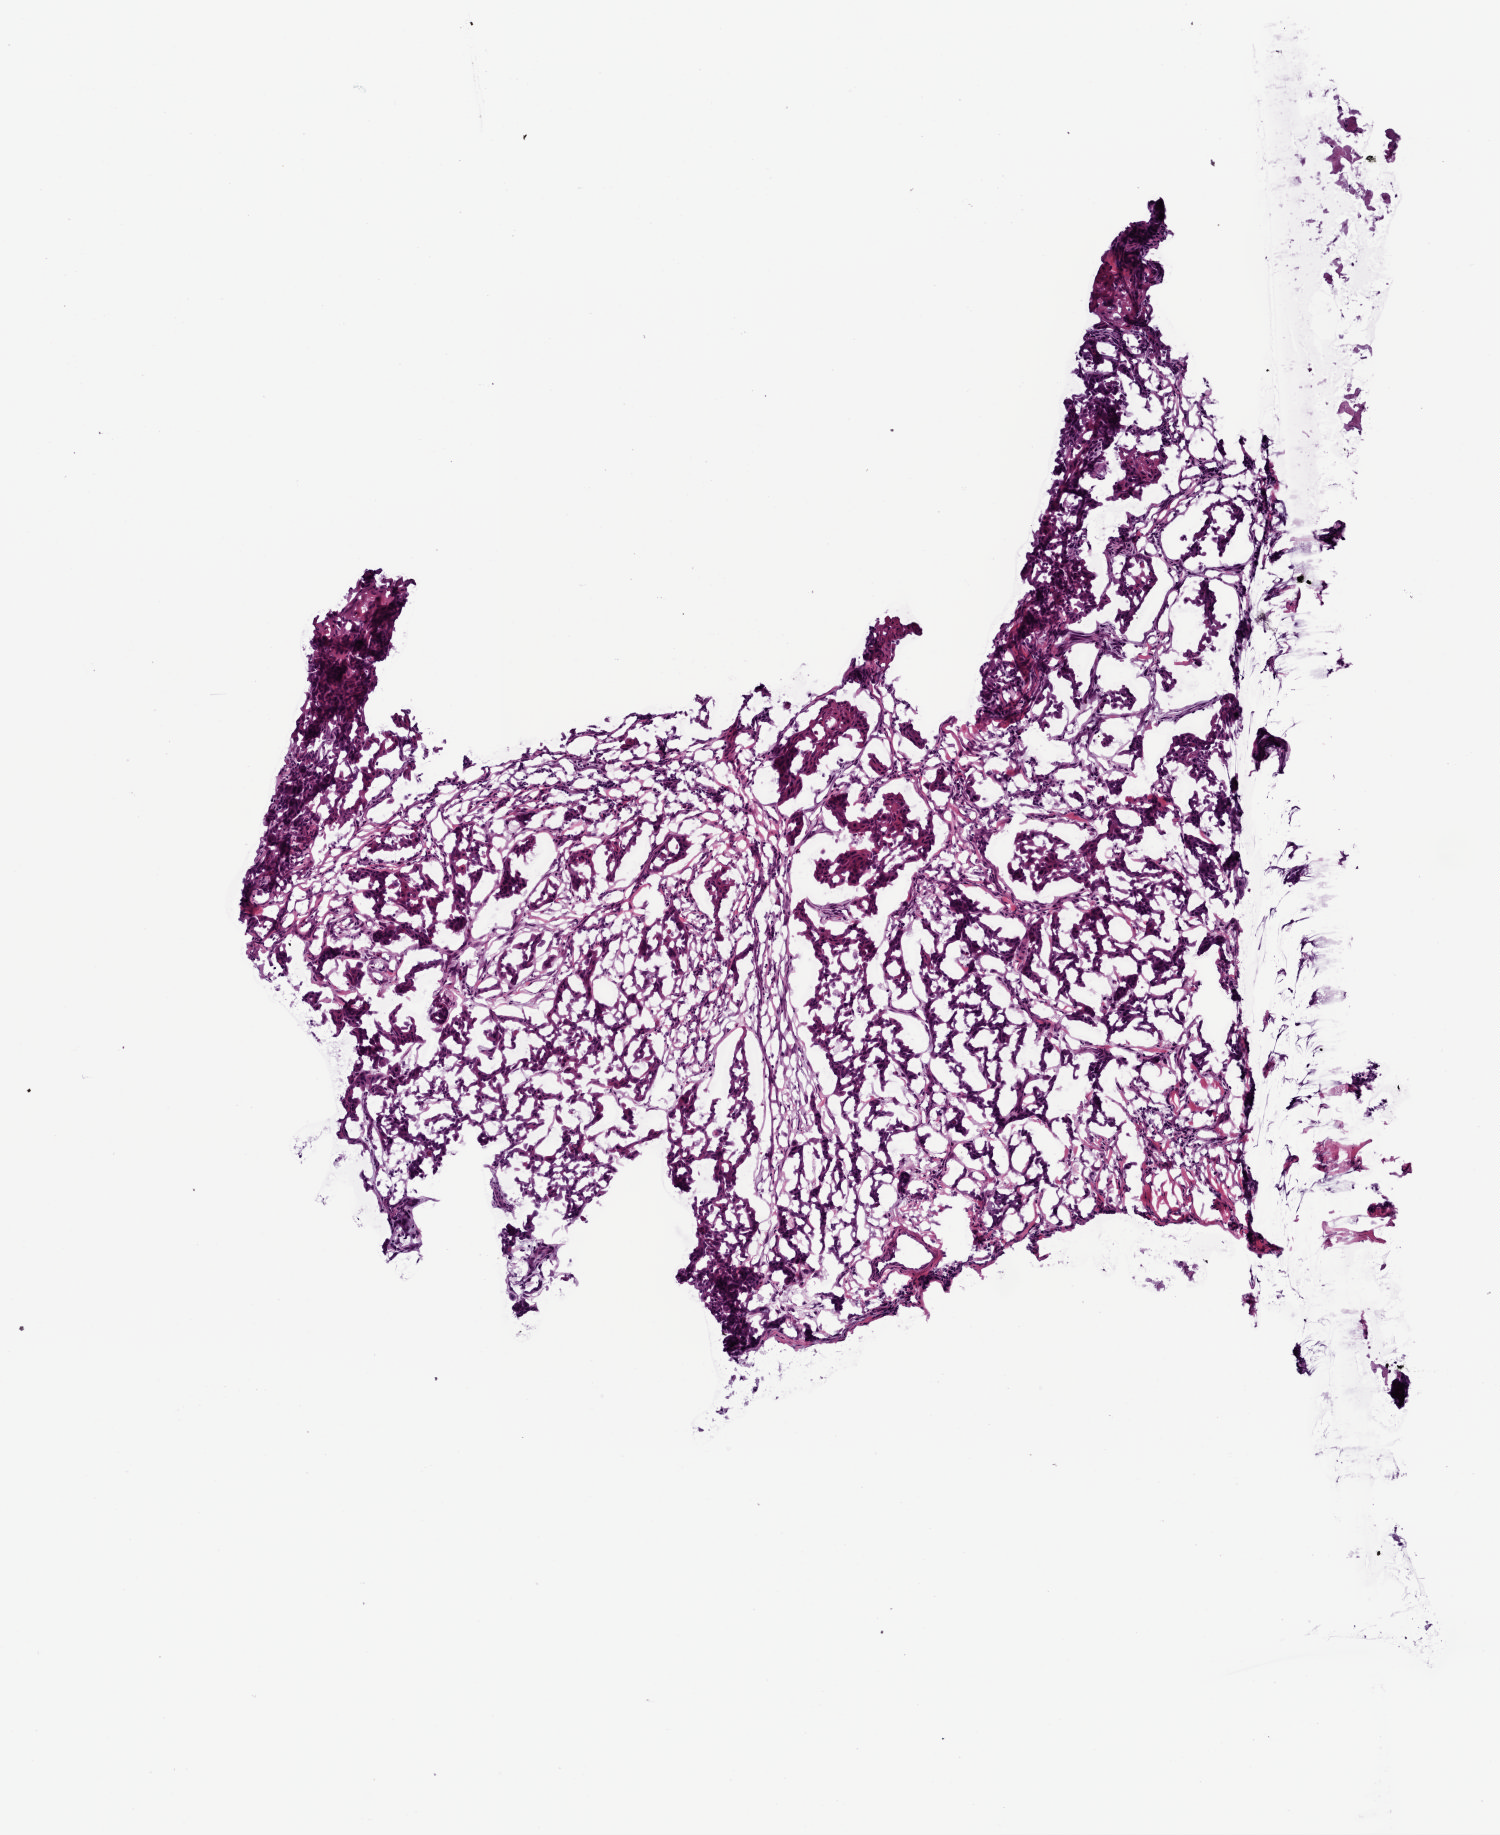
Digitized Hematoxylin and eosin (H&E) stained tissue section (whole slide) — shown as a low-resolution overview of the whole scanned area (about 3.0 x 3.7 mm, slide scanned at 20x); frozen section from the top of the tissue portion; sample: primary tumour, head and neck. Male, age 58 years at initial diagnosis. Histologic grade: G3 (poorly differentiated). Slide review estimates, as recorded: tumour cells 50%, tumour nuclei 60%, normal cells 0%, stromal cells 50%, necrosis 0%.
• TNM: T4a N2b
• pathologic diagnosis: Squamous cell carcinoma, NOS (larynx, NOS)
• AJCC pathologic stage: IVA (7th edition)